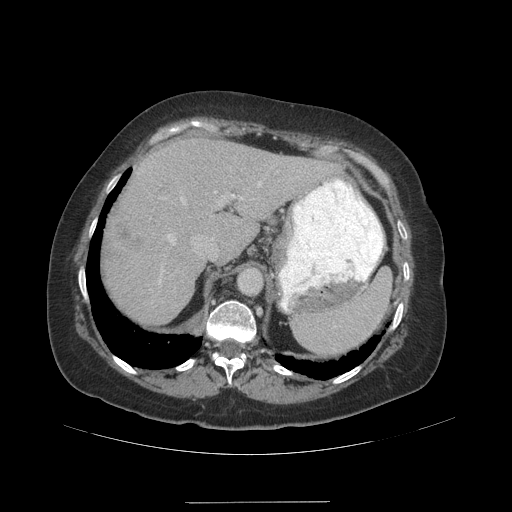
Contrast-enhanced abdominal CT (liver protocol), one axial slice. Slice 73 of 99 in the series (ordered by position). Reconstruction kernel STANDARD. 140 kVp. Soft-tissue window (W 400 / L 40 HU). 512 × 512 image matrix, field of view 440 × 440 mm. From the clinical record (not read from this slice): diagnosis: hepatocellular carcinoma (patient treated with transarterial chemoembolisation; whether this scan precedes or follows treatment is not stated here); TNM stage (as recorded): Stage-IVA; Child-Pugh class: A; tumour nodularity: multinodular.
Structures marked on this image (semi-automatically segmented with operator editing):
- abdominal aorta: bounding box (x1, y1, x2, y2) in pixels: (237, 267, 261, 295)
- liver parenchyma outside the tumour (the mass and vessels are separate outlines, so this box may not span the whole liver): (102, 138, 338, 324)
- mass: (111, 220, 141, 255)
- liver vessels: (159, 181, 262, 283)